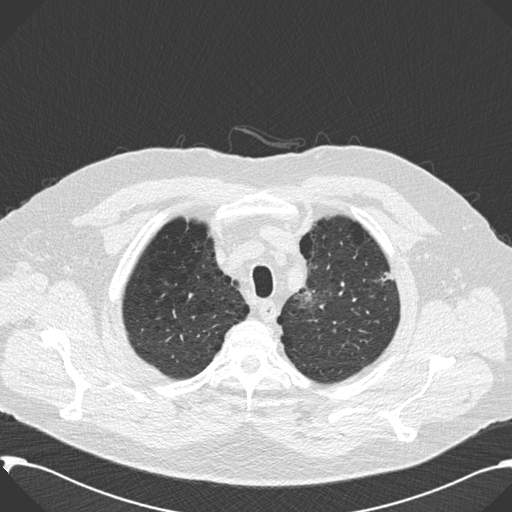
Low-dose screening chest CT, axial slice; second screening round (one year after baseline); lung window (W 1500 / L -600 HU); standard (soft-tissue) reconstruction kernel (B30f); 120 kVp; slice 27 of 199 in the series; 512 × 512 image matrix. Male, age 59 years at enrolment. Current smoker at enrolment.
- Expert reader's lesion annotation, box from (x=368, y=256) to (x=406, y=309) px.
- No non-calcified nodule or mass ≥4 mm was recorded by the screening reader at this exam.
- Official screen result: negative screen, significant abnormalities not suspicious for lung cancer.
- Later outcome: lung cancer diagnosed 518 days after this screen (after the third annual screen) — bronchiolo-alveolar carcinoma, mixed mucinous and non-mucinous, left upper lobe, stage IA (AJCC 6th edition), 20 mm at pathology.